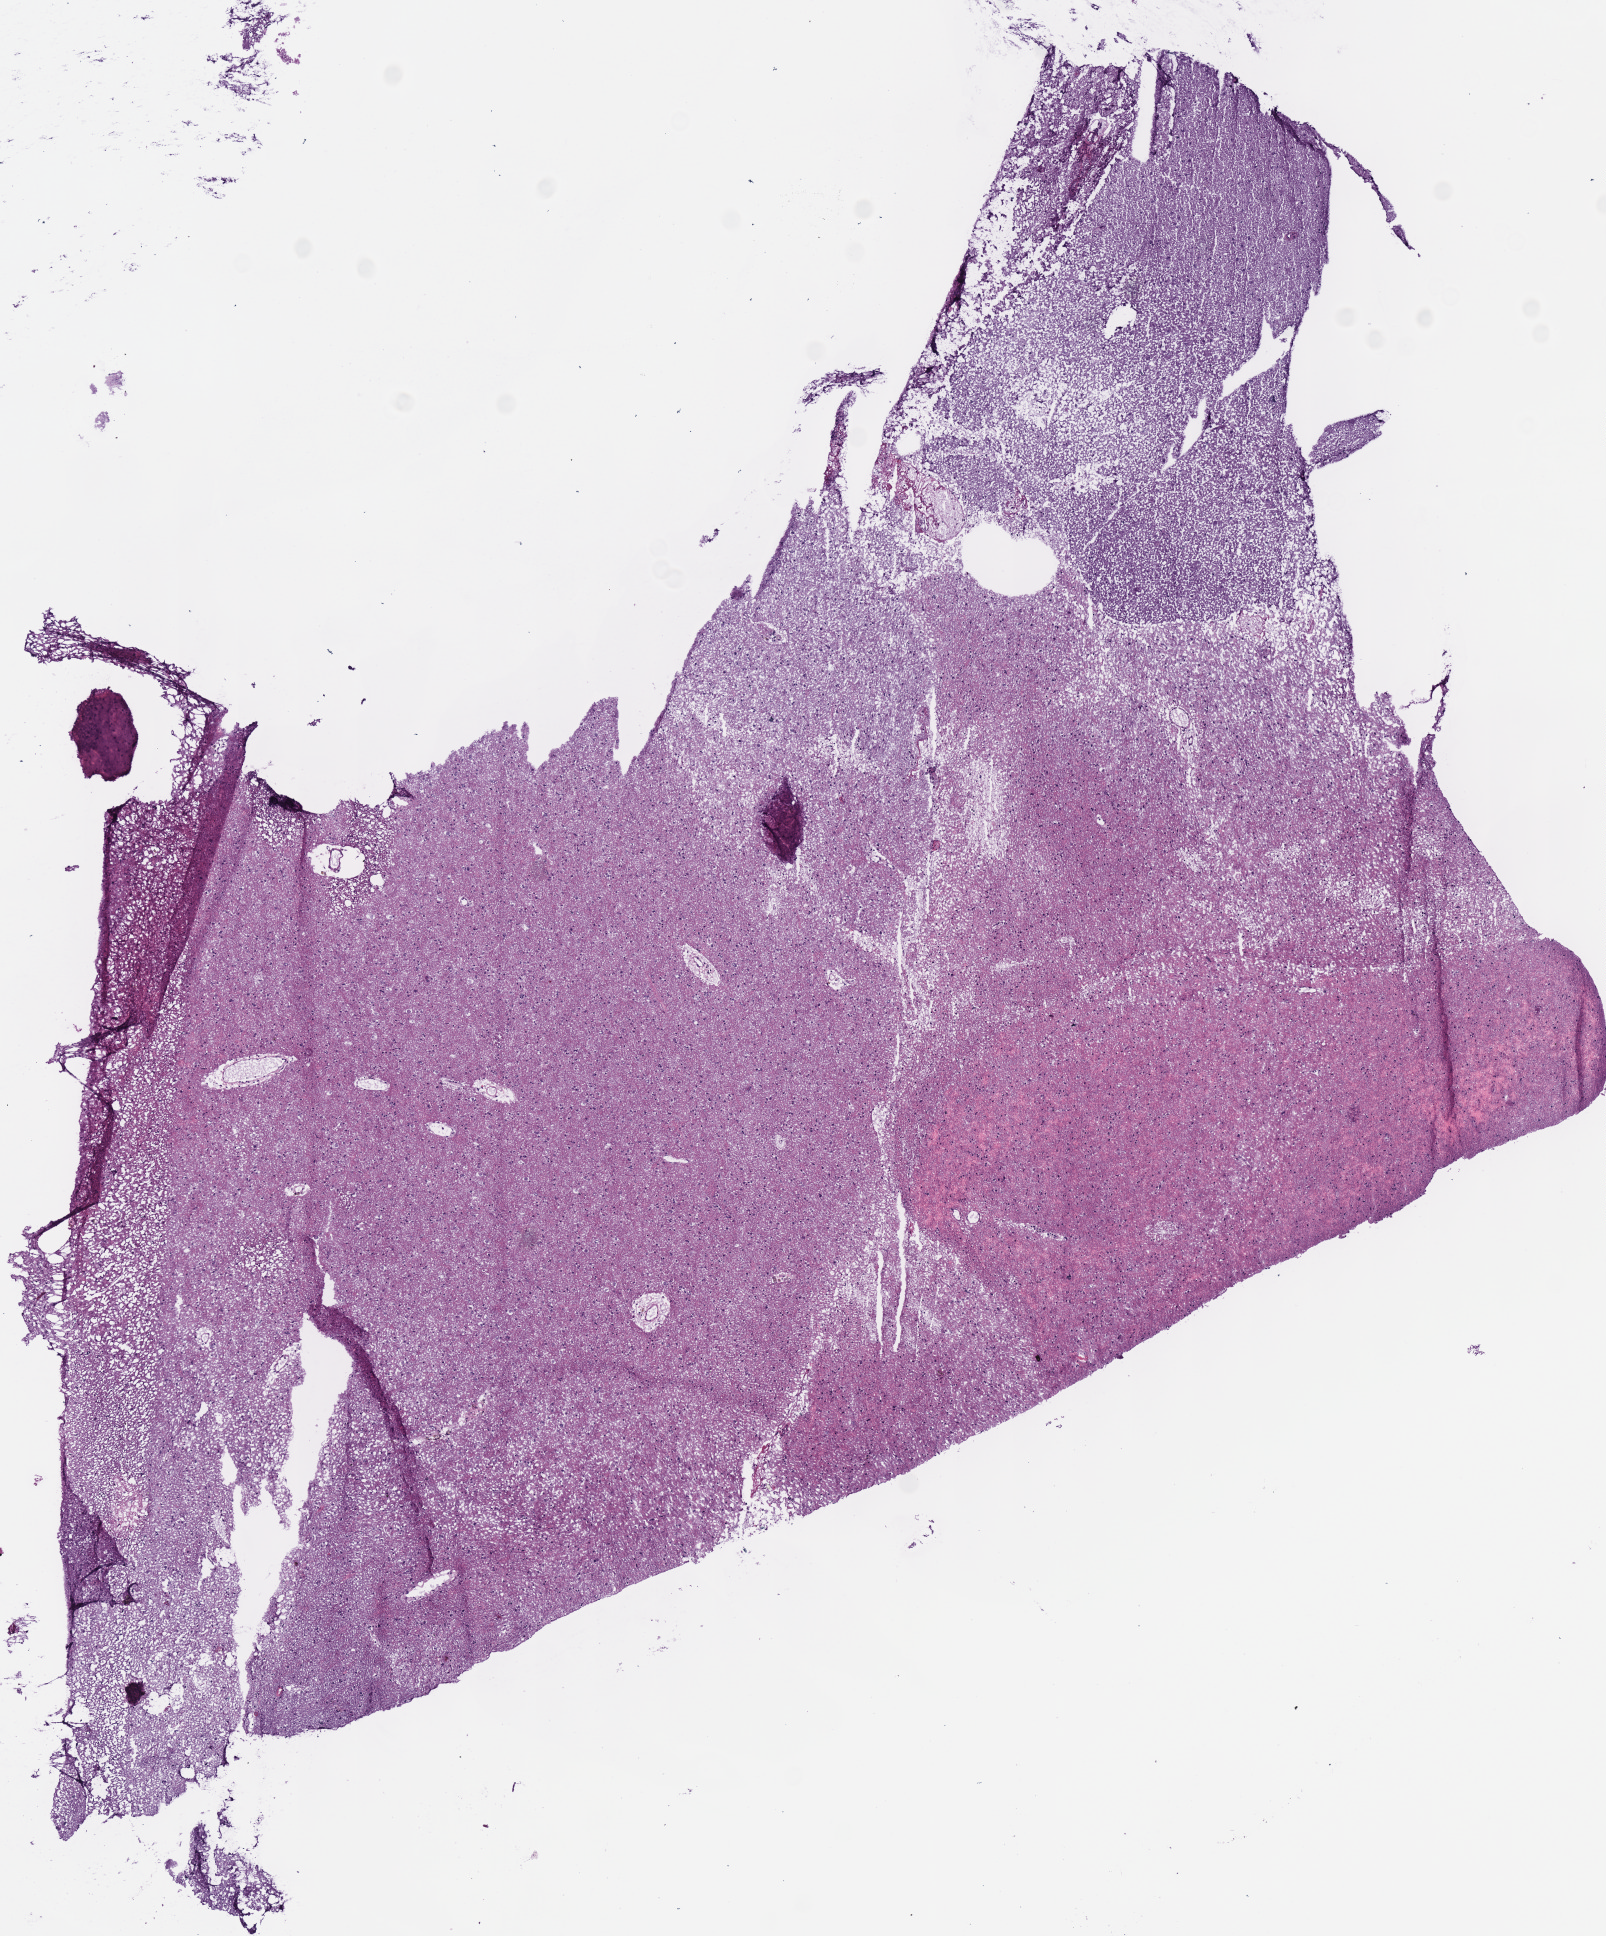
Hematoxylin and eosin (H&E) stained whole-slide image — whole scanned area (about 6.3 x 7.6 mm, from a 40x scan) shown as a low-resolution overview. Frozen section from the bottom of the tissue portion. Primary tumour sample from the brain. Female patient; age at initial diagnosis 30 years. Histologic grade: G2 (moderately differentiated). Composition of this section per pathologist review: tumour cells 90%, tumour nuclei 50%, normal cells 10%, stromal cells 0%, necrosis 0%.
• diagnosis: Mixed glioma (cerebrum)